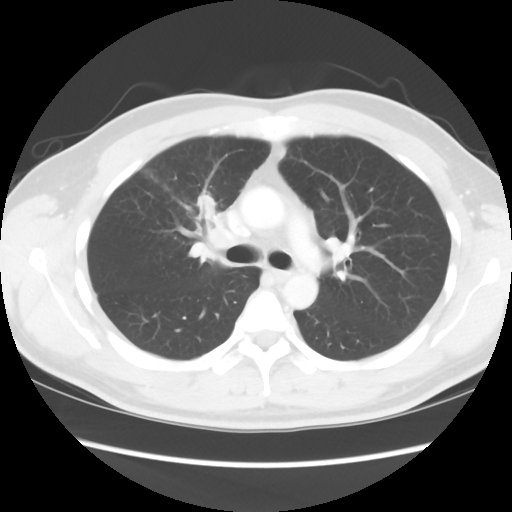
Chest CT, one axial slice; slice 60 of 80 in the series (ordered by position); 120 kVp; lung window (W 1500 / L -600 HU); 512 × 512 image matrix, field of view 360 × 360 mm. Male patient, age 35 years. From the clinical record (not read from this slice): clinical TNM (as recorded): T1c N1 M1b.
Outlined on this slice (rectangle marked by the reading radiologist):
- lung tumour (recorded histology: adenocarcinoma): bounding box (x1, y1, x2, y2) in pixels: (192, 186, 231, 263)